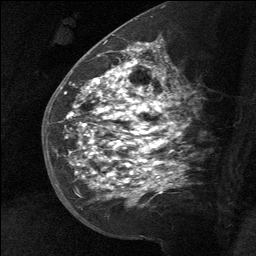
Breast MRI (dynamic contrast-enhanced), one sagittal slice. Slice 35 of 64 in the series (ordered by position). Dynamic contrast-enhanced study with each time point stored as its own series, time point 2 of 3 at this slice position (early post-contrast, ordered by acquisition time). 1.5 T. TE 4.8 ms, TR 27 ms. 2 mm slice thickness. 256 × 256 image matrix, field of view 180 × 180 mm. Female patient, age 39 years. Case-level facts recorded for this patient, not image findings: setting: breast cancer imaged before/during neoadjuvant chemotherapy; receptor status: HER2-positive.
Outlined on this slice (semi-automatically segmented with operator editing):
- analysis volume of interest (the breast-tissue region the enhancement analysis was run in; not a lesion): bounding box (x1, y1, x2, y2) in pixels: (58, 40, 165, 217)
- tumour enhancement mask (voxels above the 90 % enhancement threshold inside the analysis volume of interest): (67, 42, 158, 197)